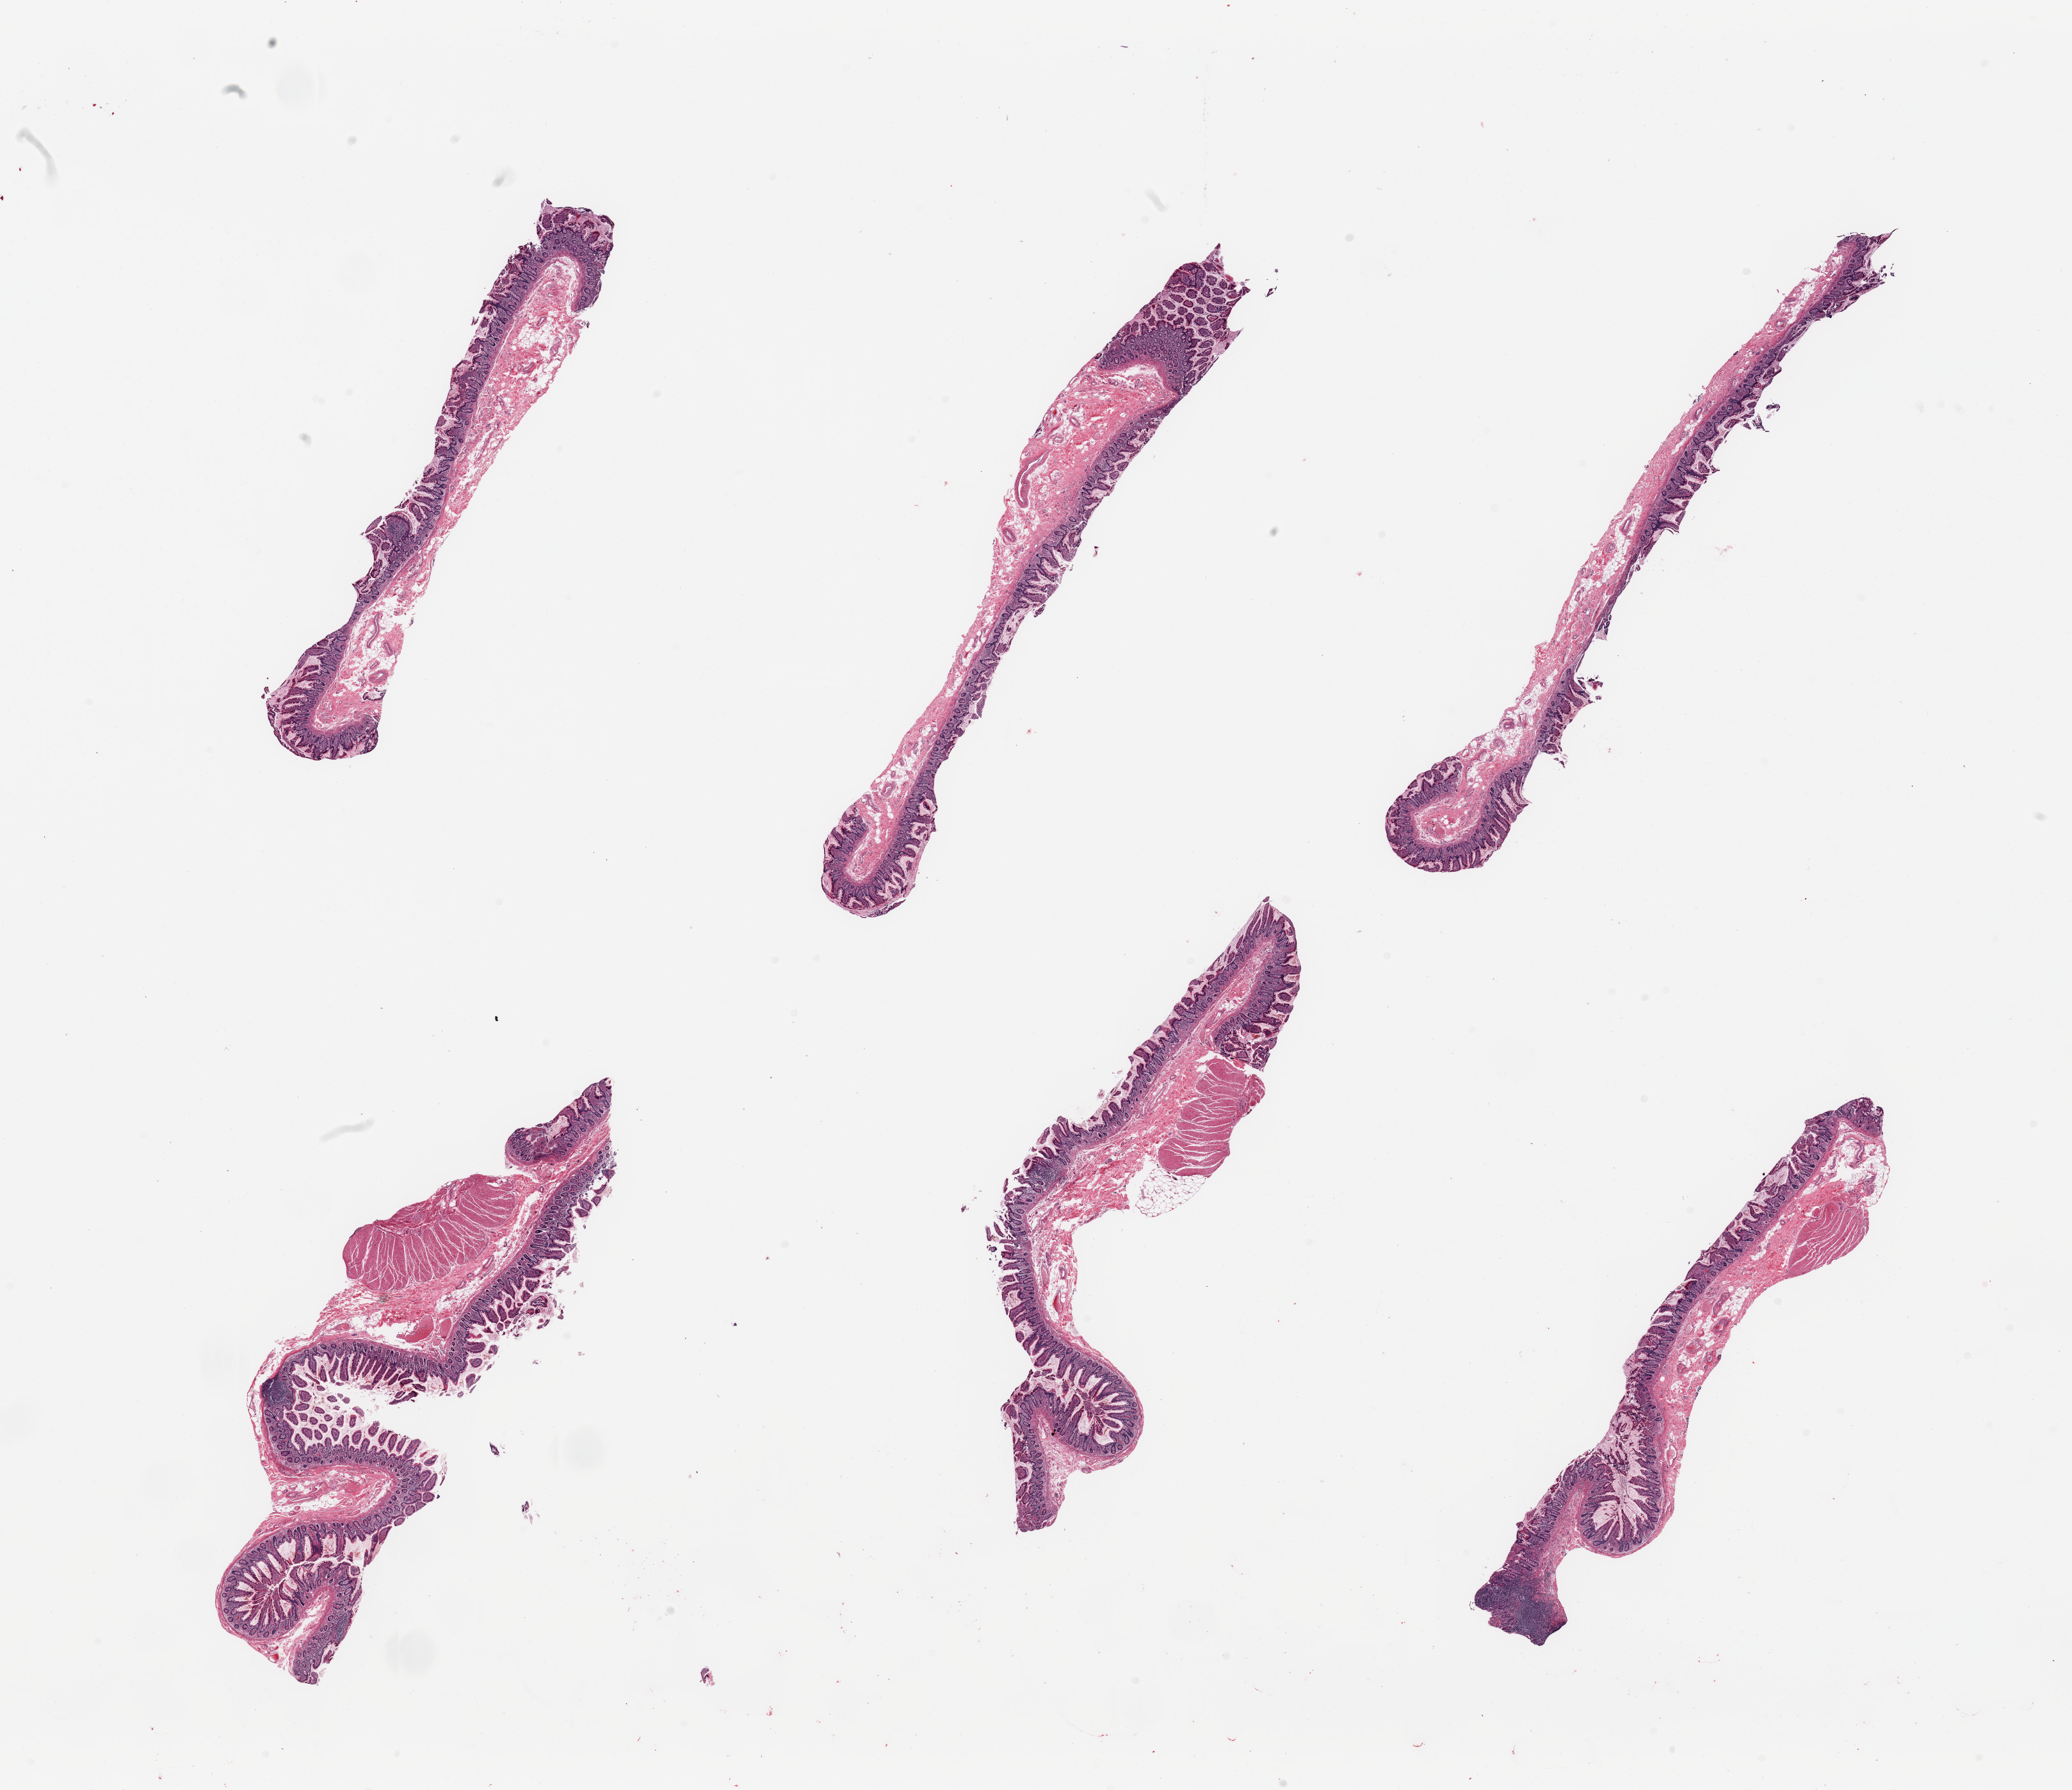
Haematoxylin and eosin whole-slide image, brightfield — a low-resolution overview of the entire scanned area, about 25.6 x 22.1 mm. PAXgene-fixed paraffin-embedded (PFPE) section. Target tissue: ileum. Tissue donor sample.
Reviewer comment on this tissue sample: 6 pieces; predominantly mucosa with few strips of residual muscularis (not target) and only rare lymphoid aggregate.